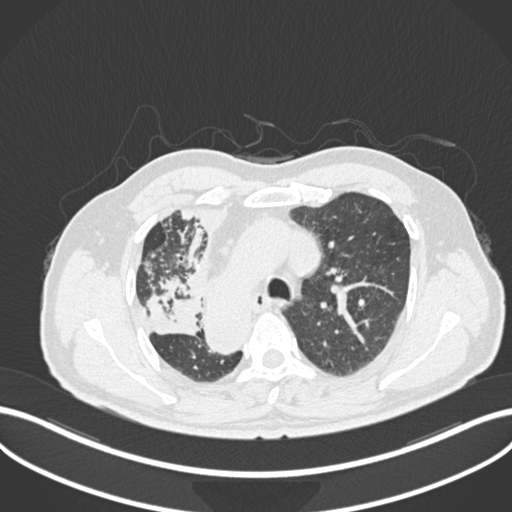
Chest CT, one axial slice; reconstruction kernel B30f; 120 kVp; lung window (W 1500 / L -600 HU); 1 mm slice thickness; 512 × 512 image matrix. Male patient, age 67 years. From the clinical record (not read from this slice): clinical TNM (as recorded): T2a N0 M0.
Annotated regions visible in this slice (rectangle marked by the reading radiologist):
- lung tumour (recorded histology: squamous cell carcinoma): box from (x=144, y=278) to (x=202, y=338) px